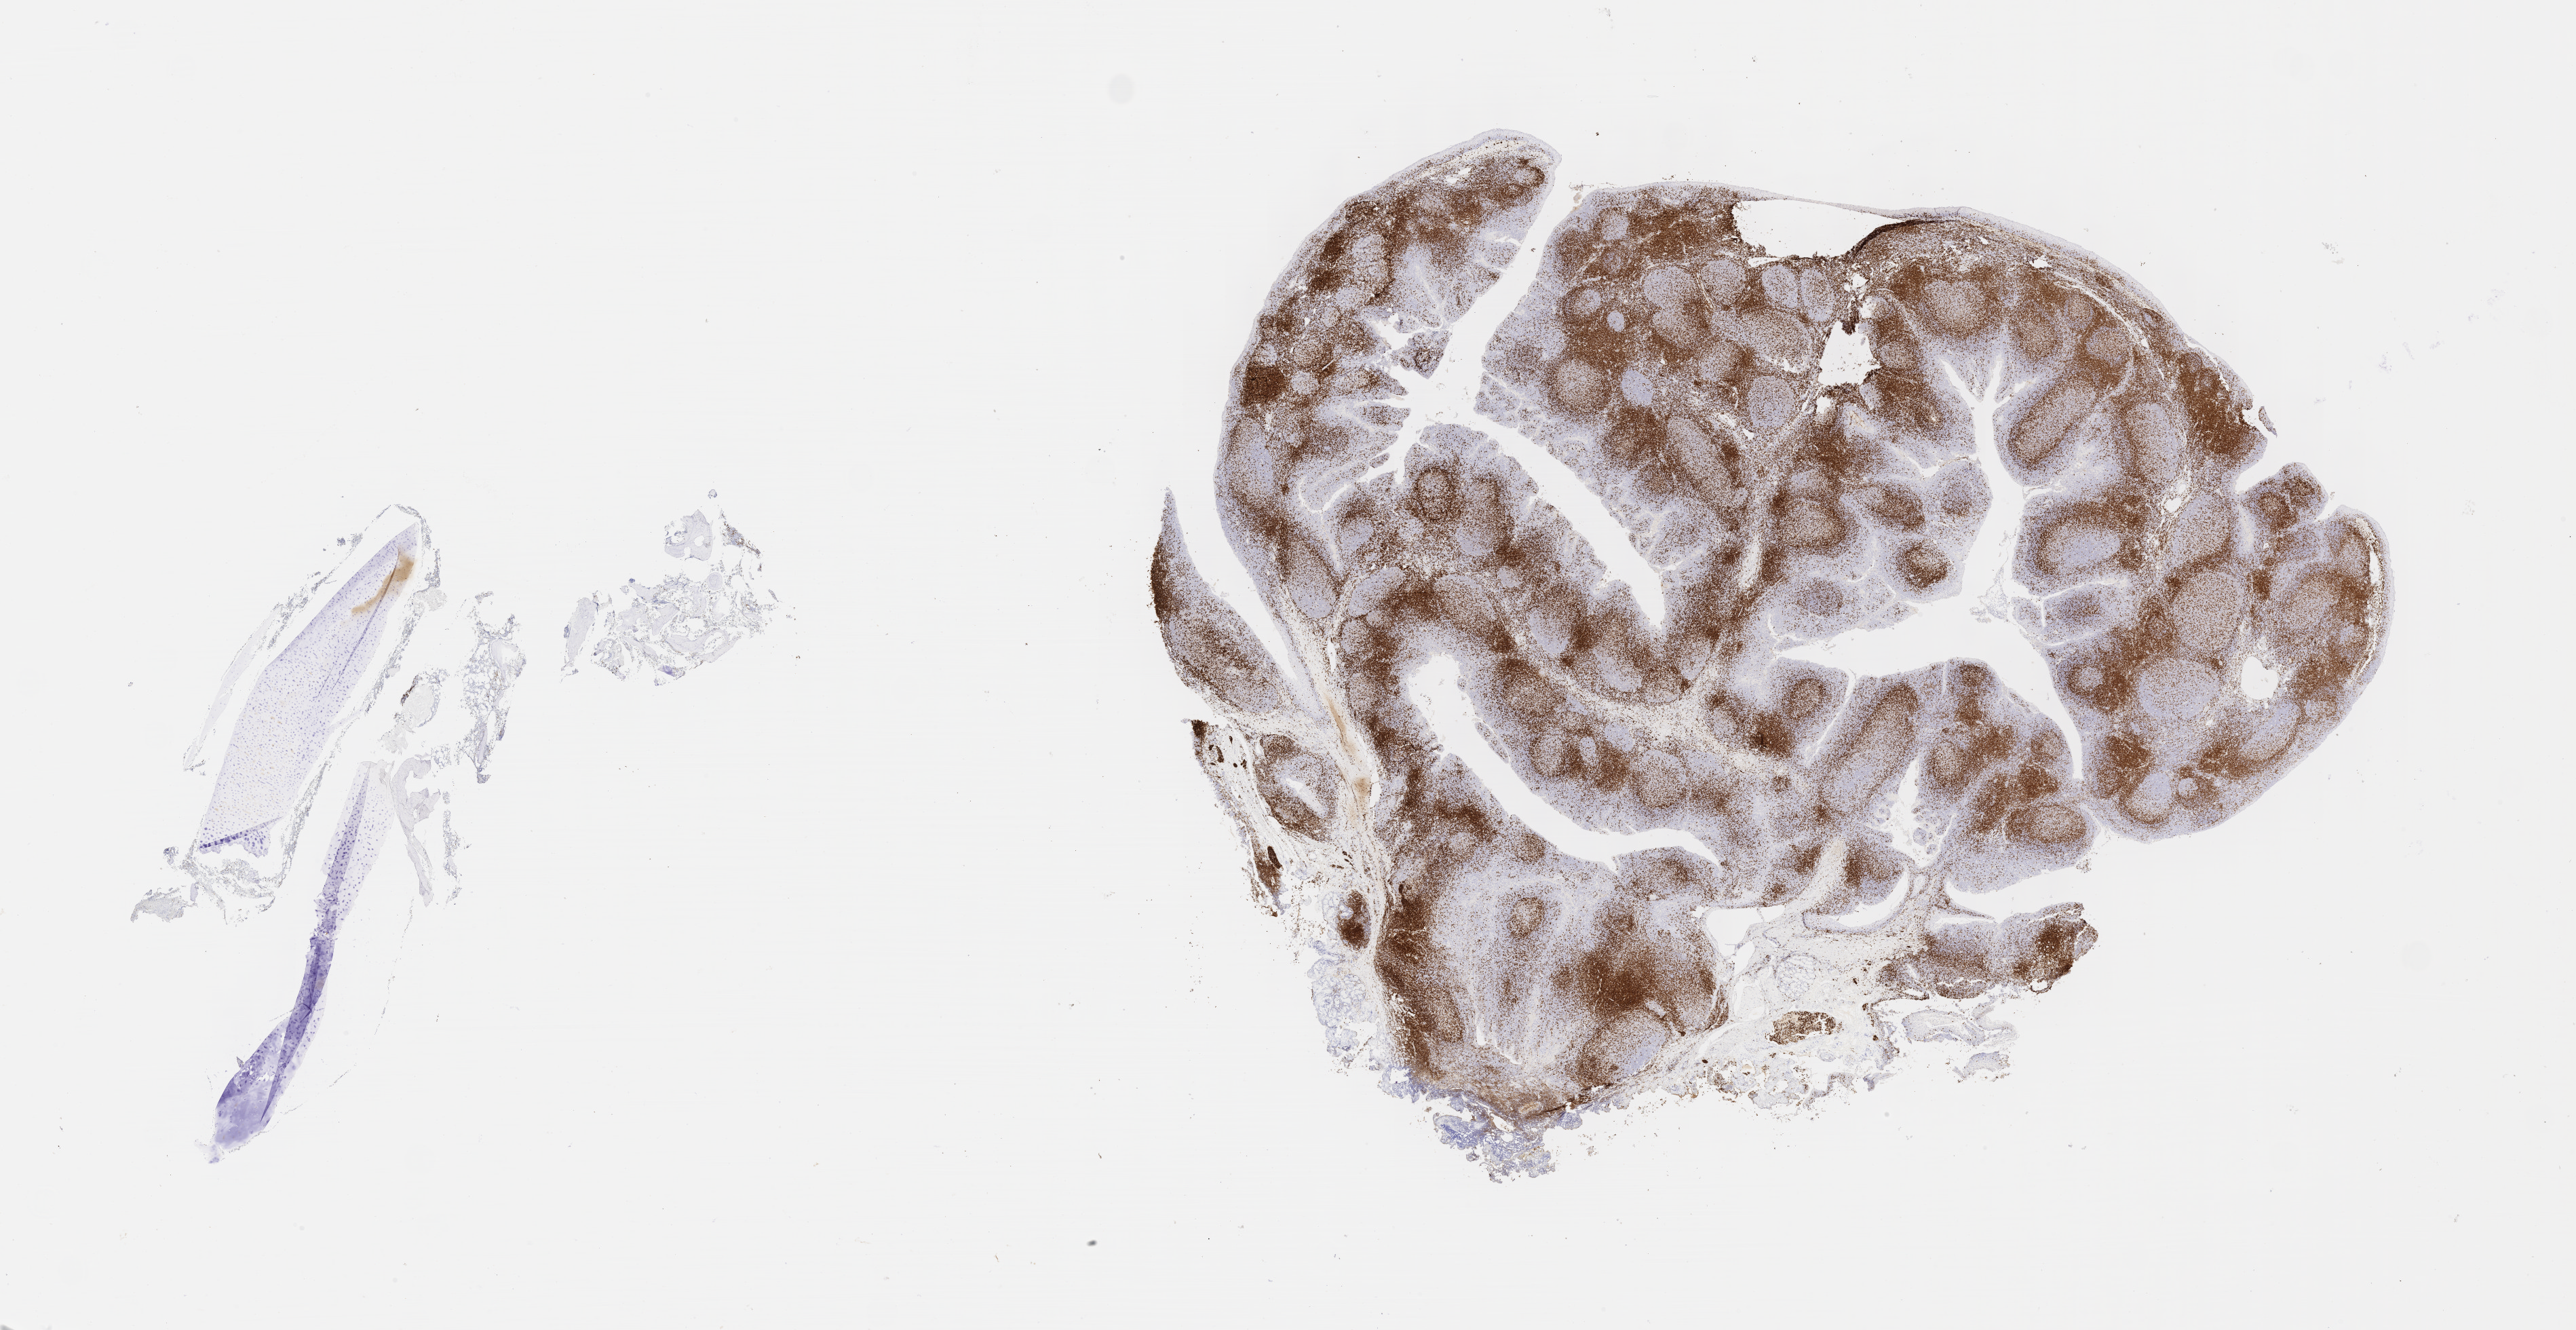
Immunohistochemistry (IHC) whole-slide image stained for CD3, a low-resolution overview of the entire scanned area, about 30.7 x 15.8 mm; specimen: tumor tissue; site: bone marrow. Patient female; age 11 years.
Histologic diagnosis: Burkitt lymphoma, NOS.